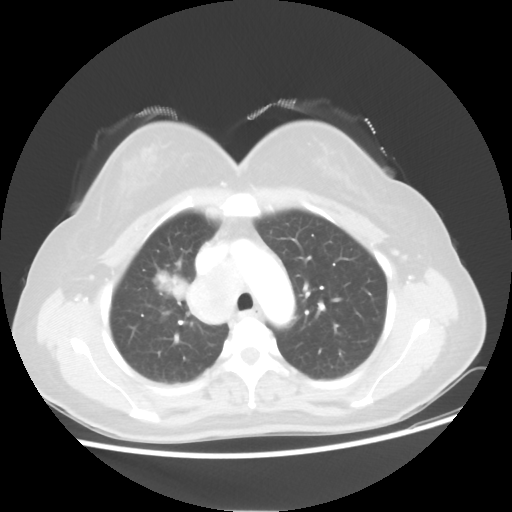
Chest CT, one axial slice. Slice 37 of 50 in the series (ordered by position). 100 kVp. Lung window (W 1500 / L -600 HU). 5 mm slice thickness. 512 × 512 image matrix. Patient: female, 40 years. From the clinical record (not read from this slice): clinical TNM (as recorded): T1c N3 M0; histopathological grade: G3.
Outlined on this slice (rectangle marked by the reading radiologist):
- lung tumour (recorded histology: small cell carcinoma): bounding box <153,264,184,309> (left, top, right, bottom; pixels)